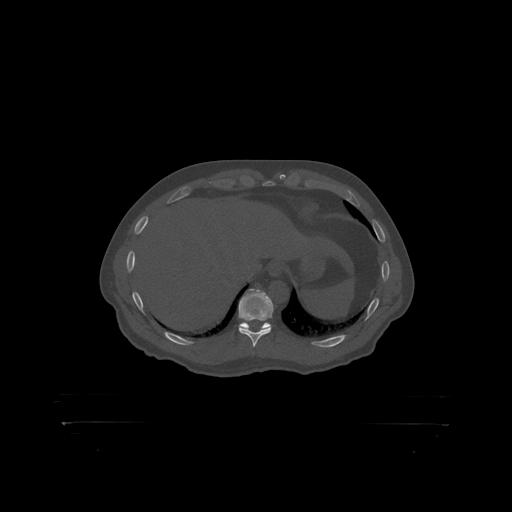
CT including the spine, one axial slice; slice 394 of 399 in the series (ordered by position); reconstruction kernel STANDARD; bone window (W 1800 / L 400 HU); 1.25 mm slice thickness; 512 × 512 image matrix, field of view 650 × 650 mm. Patient: male, 46 years. From the clinical record (not read from this slice): primary cancer: skin.
Outlined on this slice (semi-automatic segmentation, software-assisted and operator-edited):
- T10 vertebra: bounding box (x1, y1, x2, y2) in pixels: (239, 290, 273, 319)